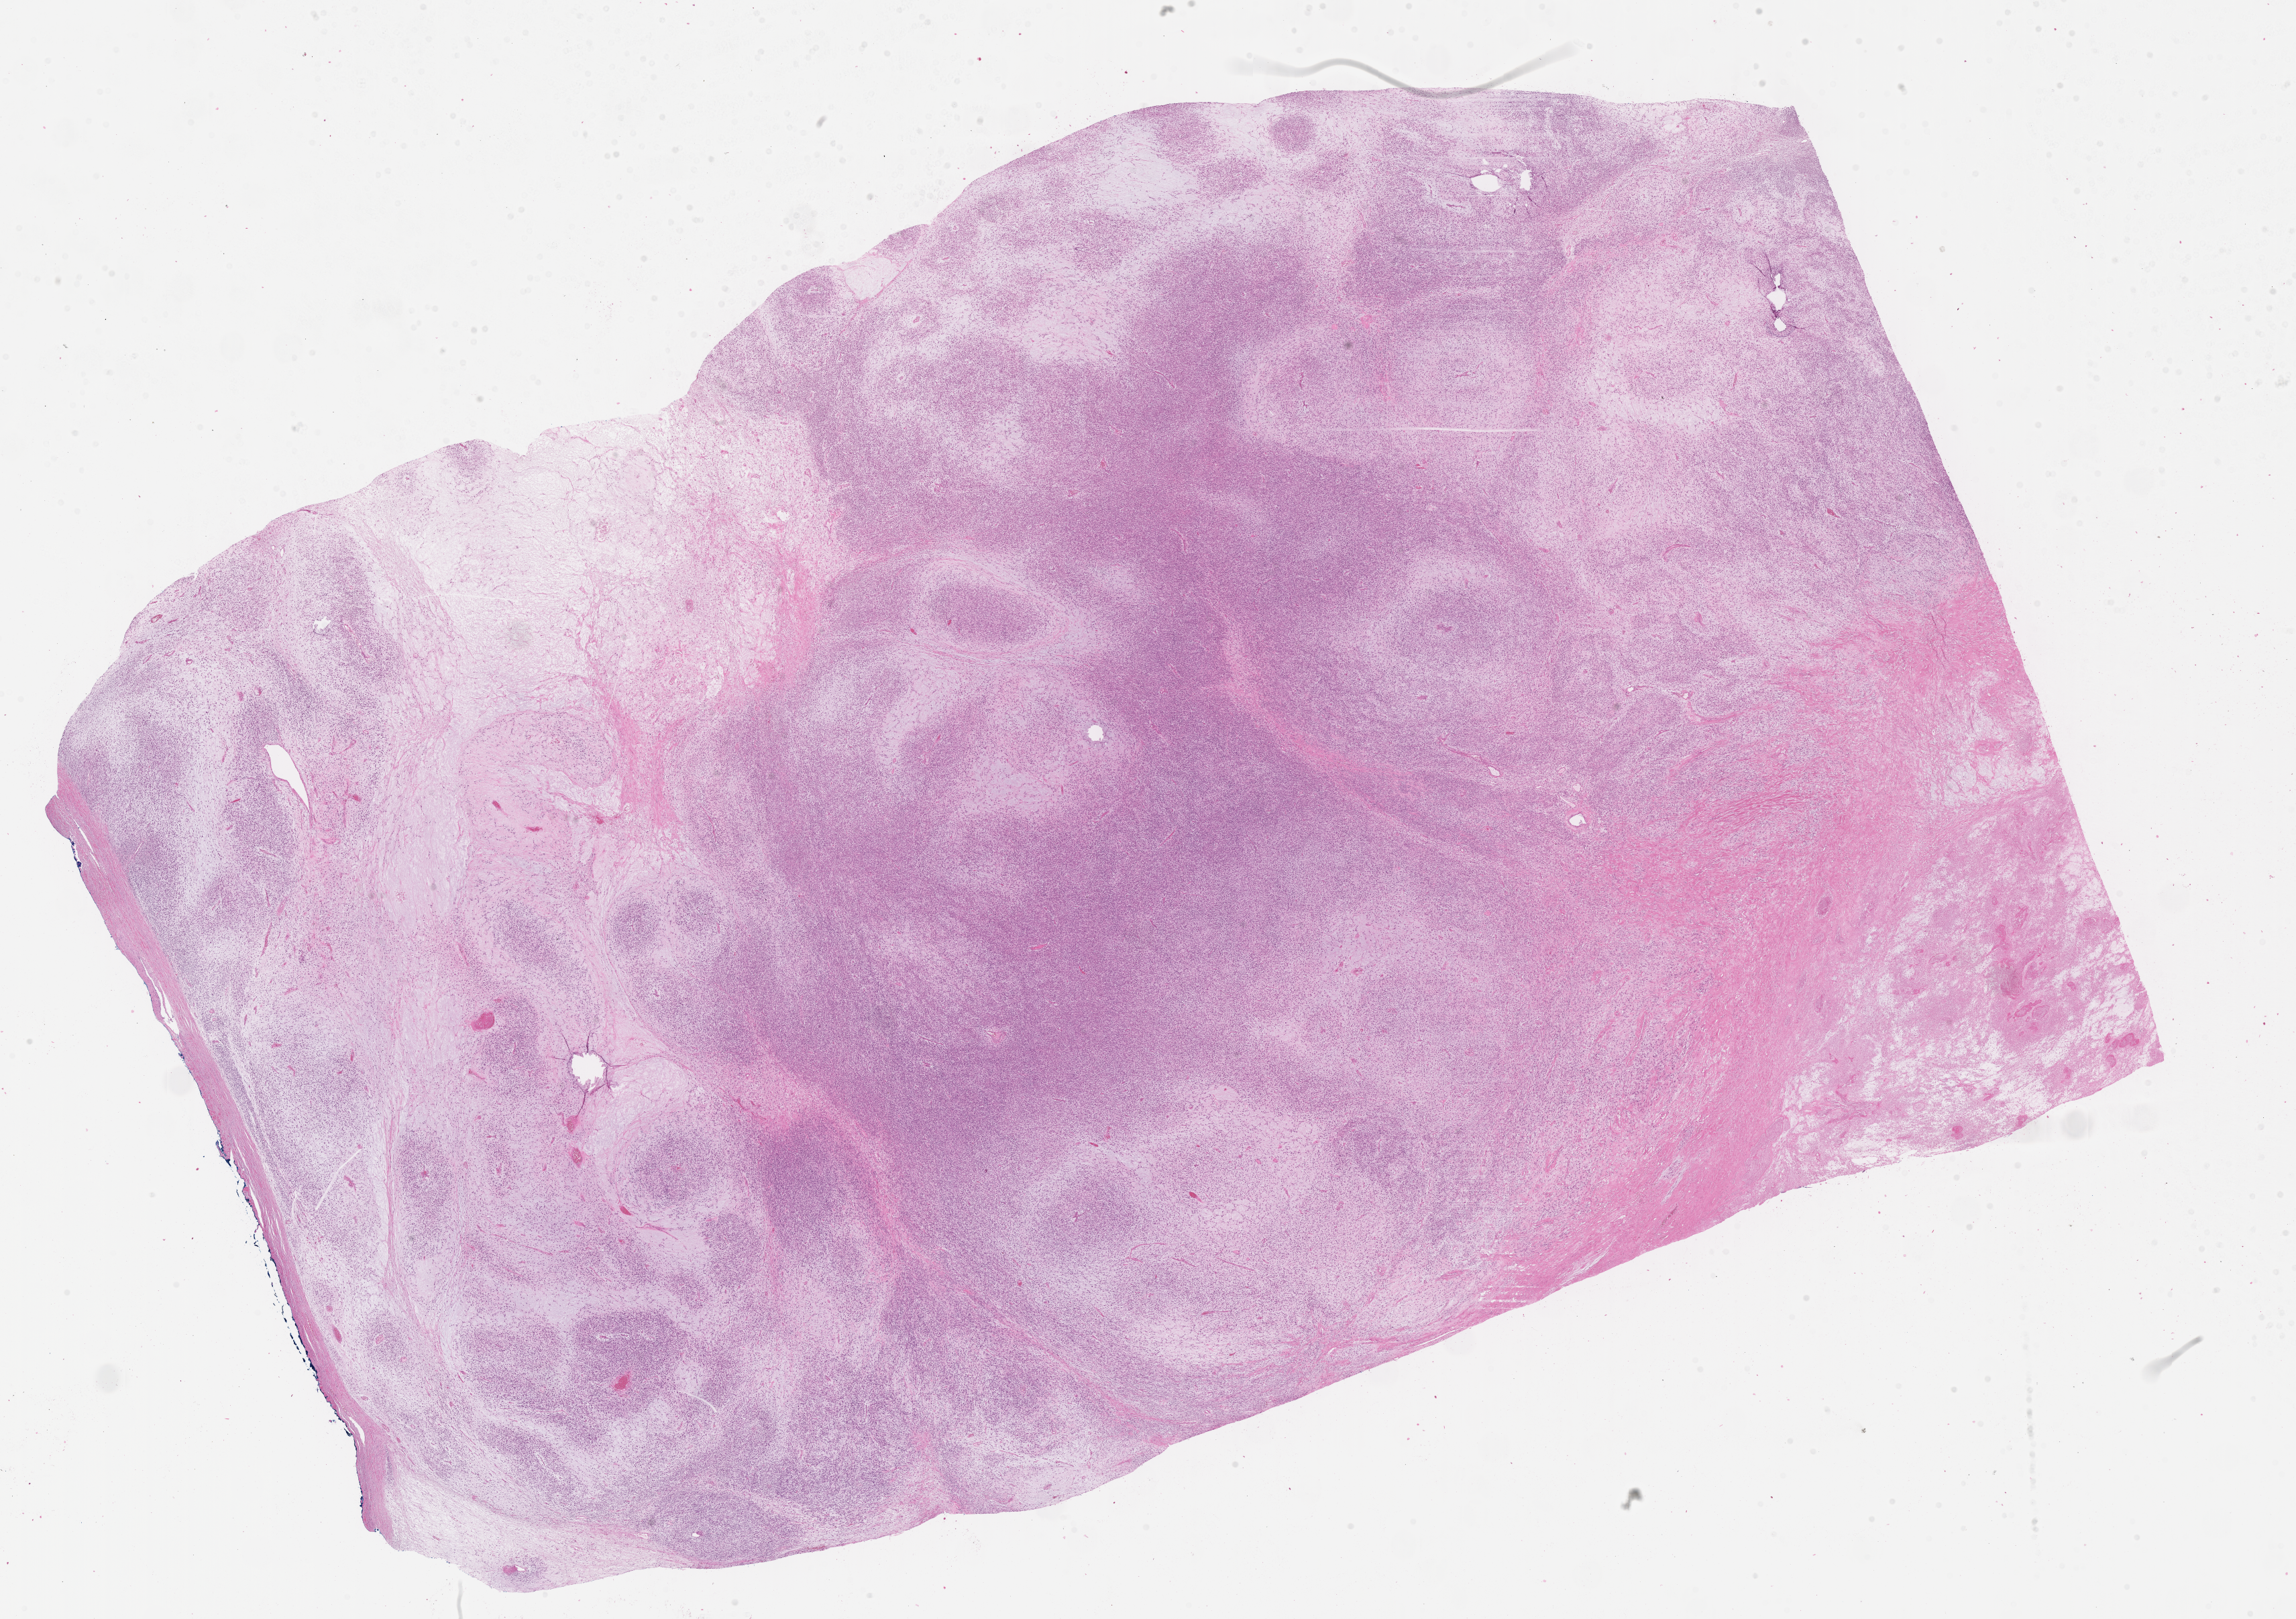
Whole-slide image, H&E stain of tumor tissue, a low-resolution overview of the entire scanned area, about 27.7 x 19.5 mm; formalin-fixed paraffin-embedded section; sample anatomic site: testicle-left. Patient: male, age 8.9 years at diagnosis.
- diagnosis: rhabdomyosarcoma; histological classification: embryonal rhabdomyosarcoma
- stage (as recorded): 1
- primary site (case record): testis-Paratestis